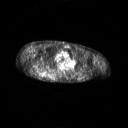
FDG PET of an extremity soft-tissue mass (from a PET/CT study), one axial slice. Slice 181 of 267 in the series (ordered by position). 128 × 128 image matrix, field of view 700 × 700 mm. Patient: male, 61 years. From the clinical record (not read from this slice): histological type: pleiomorphic spindle cell undifferentiated; grade: high; site of the primary tumour: right parascapusular.
Outlined on this slice (expert contour drawn on MRI and transferred to this co-registered scan by the dataset authors):
- gross tumour volume including surrounding oedema: box from (x=34, y=69) to (x=58, y=78) px
- gross tumour volume (mass): (x=39, y=70)–(x=47, y=77)